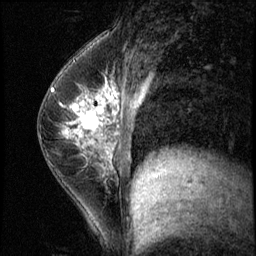
Breast MRI (dynamic contrast-enhanced), one sagittal slice. Position 31 of 56 along the scan axis. 3 images stored at this slice position (order not interpretable as contrast timing). 1.5 T. TE 4.2 ms, TR 8.7 ms. 2.5 mm slice thickness. 256 × 256 image matrix. Female patient, age 35 years. Case-level facts recorded for this patient, not image findings: setting: breast cancer imaged before/during neoadjuvant chemotherapy; receptor status: HER2-positive.
Annotated regions visible in this slice (semi-automatically segmented with operator editing):
- analysis volume of interest (the breast-tissue region the enhancement analysis was run in; not a lesion): box from (x=58, y=84) to (x=138, y=186) px
- tumour enhancement mask (voxels above the 140 % enhancement threshold inside the analysis volume of interest): (x=63, y=84)–(x=138, y=144)